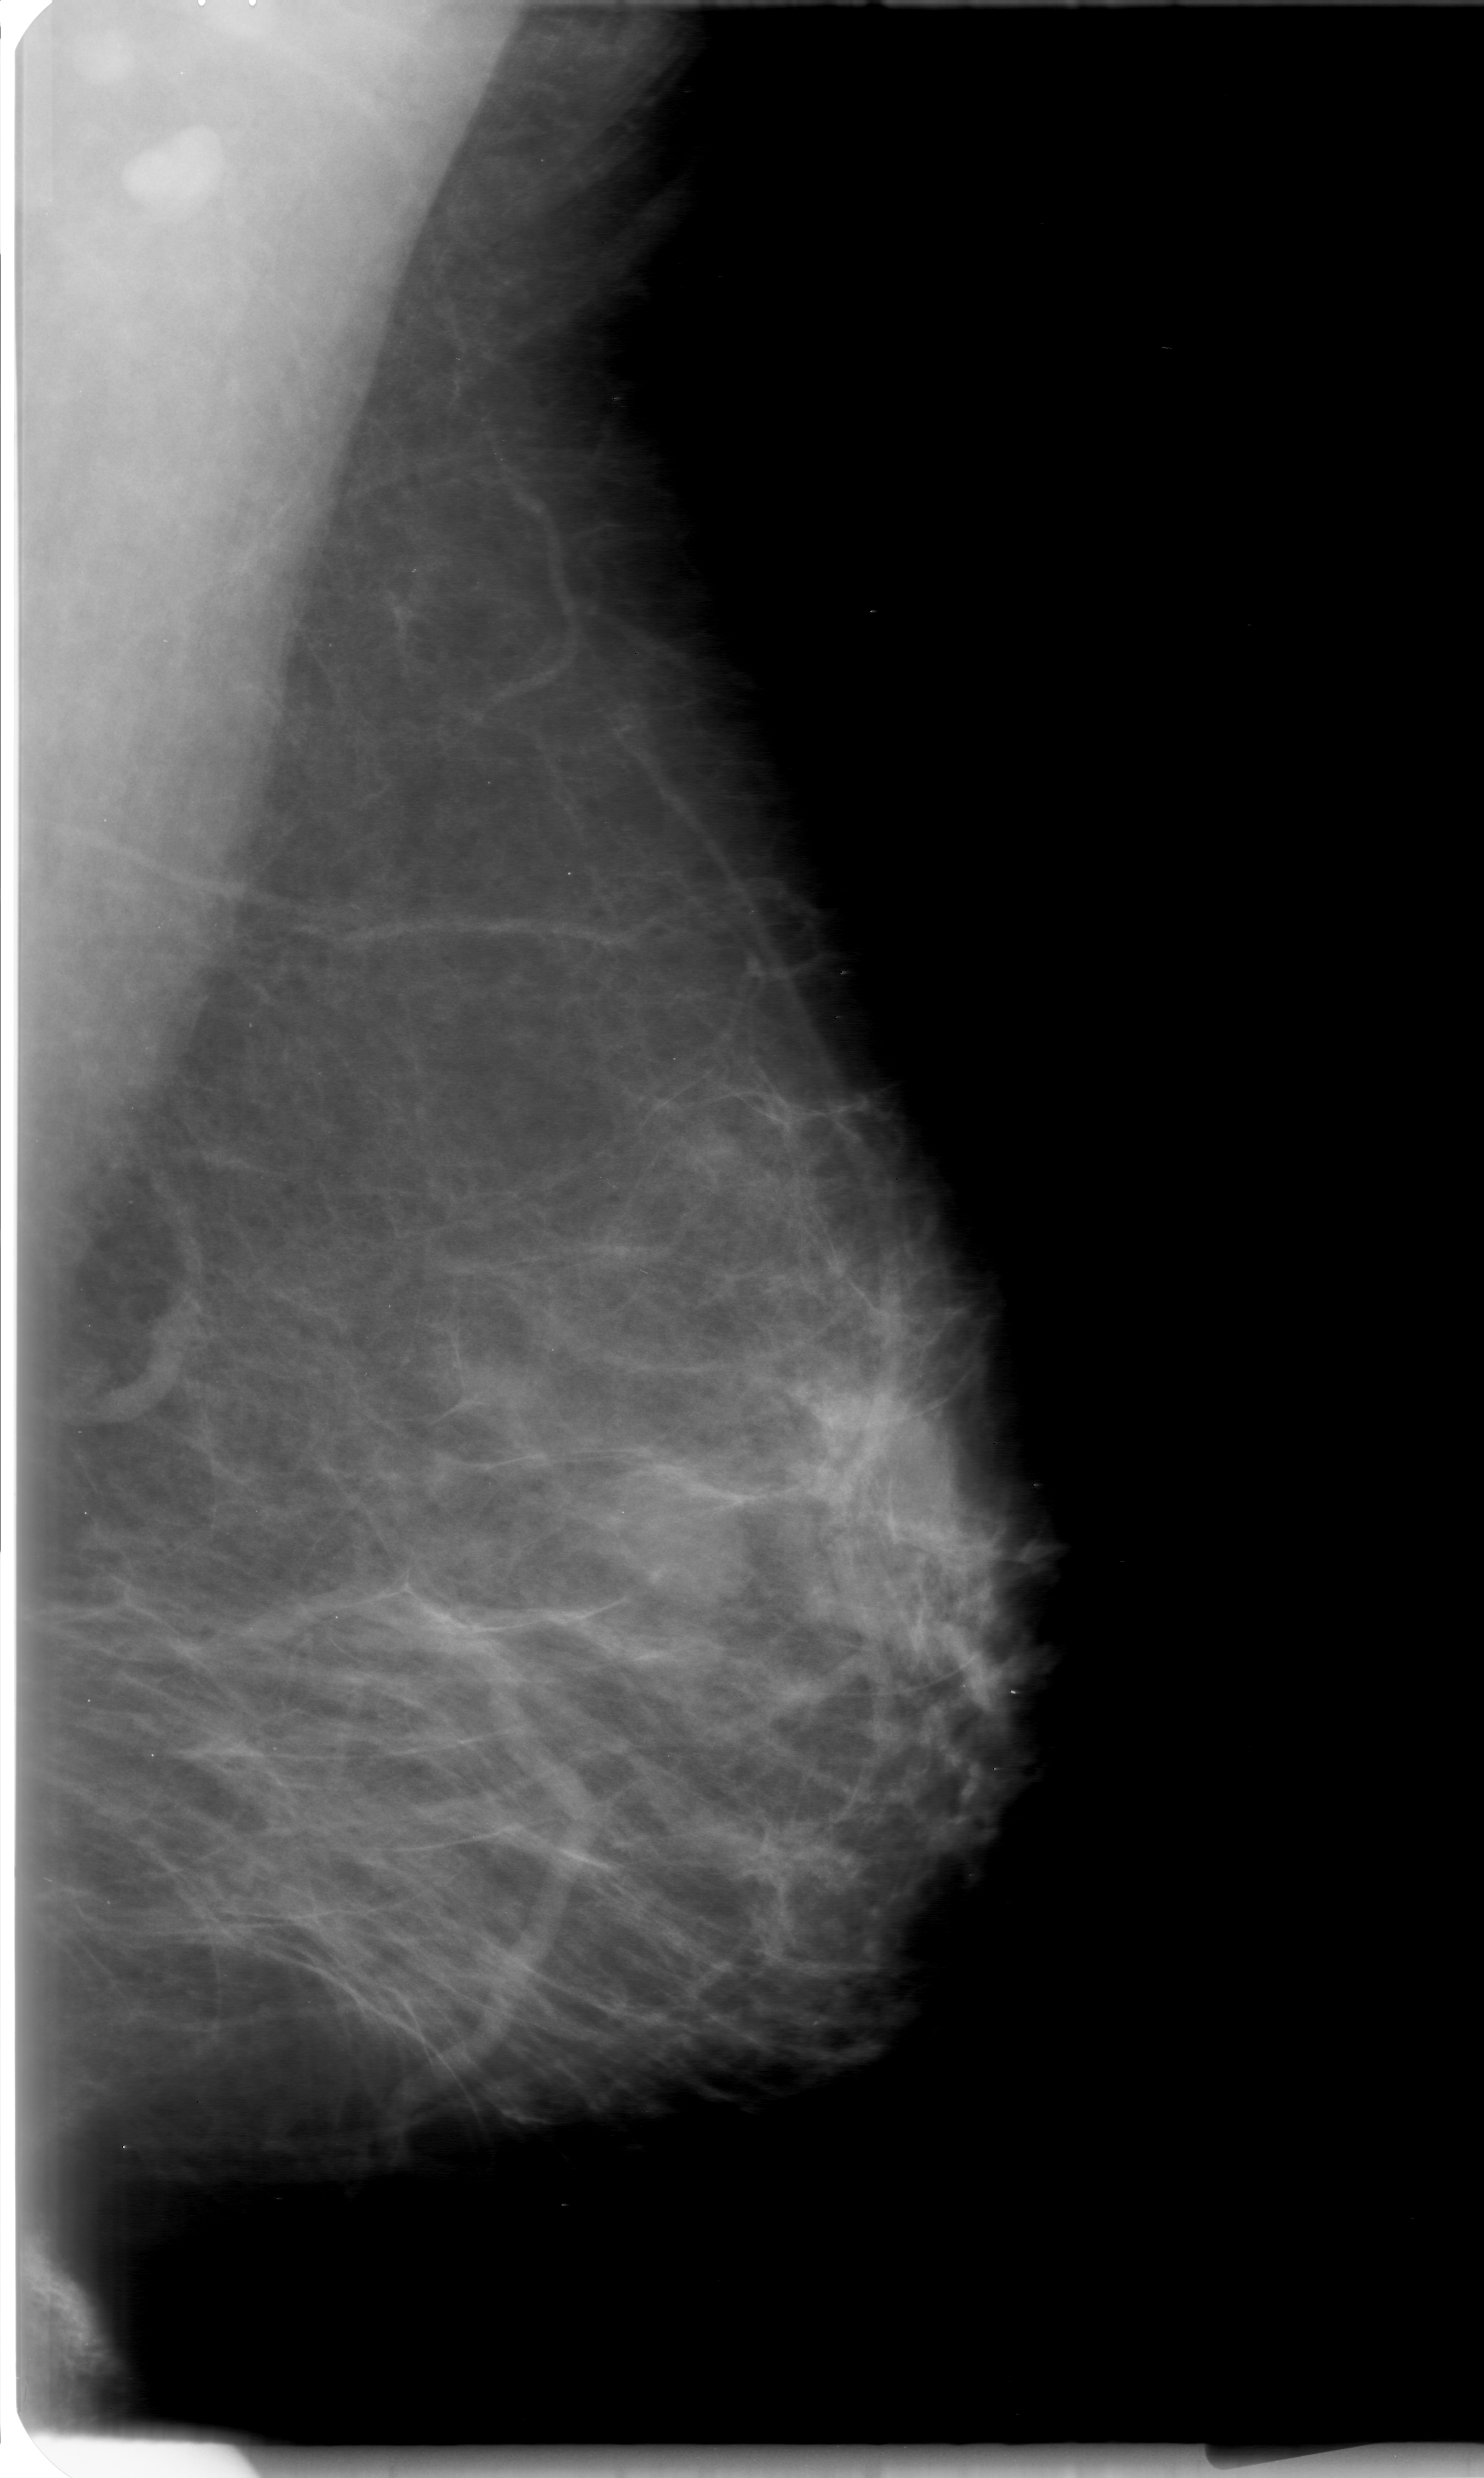
Mammogram (digitized film); left breast; MLO view; breast composition: scattered fibroglandular densities (BI-RADS density category 2 of 4).
Abnormality record for this image: mass, shape oval, margins obscured; BI-RADS assessment category 0; subtlety rating 4 on a 1 (subtle) to 5 (obvious) scale; pathology (as recorded): benign.